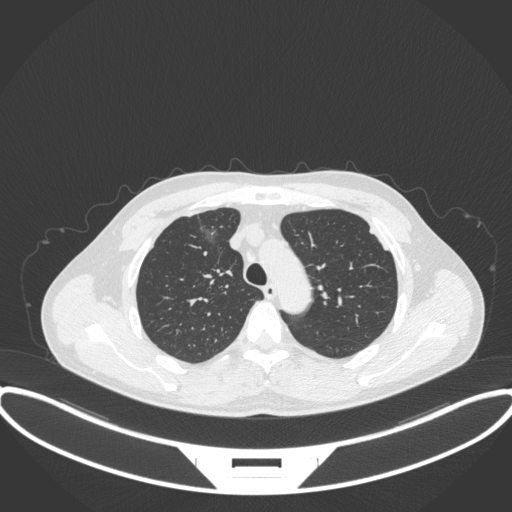
Chest CT, one axial slice. Position 274 of 395 along the scan axis. Reconstruction kernel B31f. 120 kVp. Lung window (W 1500 / L -600 HU). 1 mm slice thickness. 512 × 512 image matrix, field of view 424 × 424 mm. Male patient, age 60 years. From the clinical record (not read from this slice): clinical TNM (as recorded): T1c N0 M0.
Outlined on this slice (bounding box drawn by a radiologist):
- lung tumour (recorded histology: adenocarcinoma): bounding box [x1, y1, x2, y2] px = [190, 210, 225, 250]